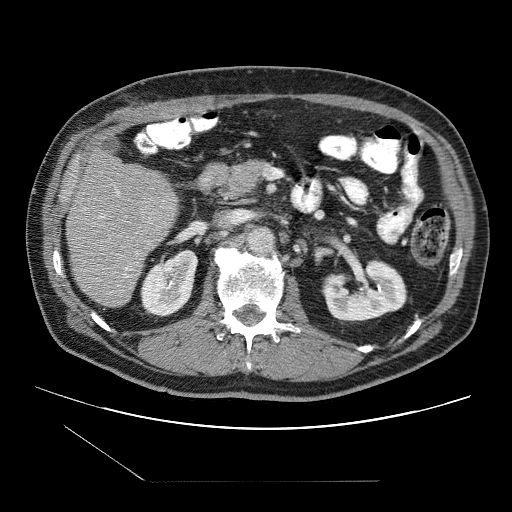
Contrast-enhanced abdominal CT (liver protocol), one axial slice. Position 38 of 109 along the scan axis. Reconstruction kernel STANDARD. 120 kVp. One of 2 acquisitions stored at this slice position. Soft-tissue window (W 400 / L 40 HU). 2.5 mm slice thickness. 512 × 512 image matrix, field of view 400 × 400 mm. From the clinical record (not read from this slice): diagnosis: hepatocellular carcinoma (patient treated with transarterial chemoembolisation; whether this scan precedes or follows treatment is not stated here); TNM stage (as recorded): Stage-IIIB.
Annotated regions visible in this slice (semi-automatically segmented with operator editing):
- liver parenchyma outside the tumour (the mass and vessels are separate outlines, so this box may not span the whole liver): box from (x=66, y=152) to (x=178, y=306) px
- liver vessels: (x=98, y=189)–(x=148, y=277)